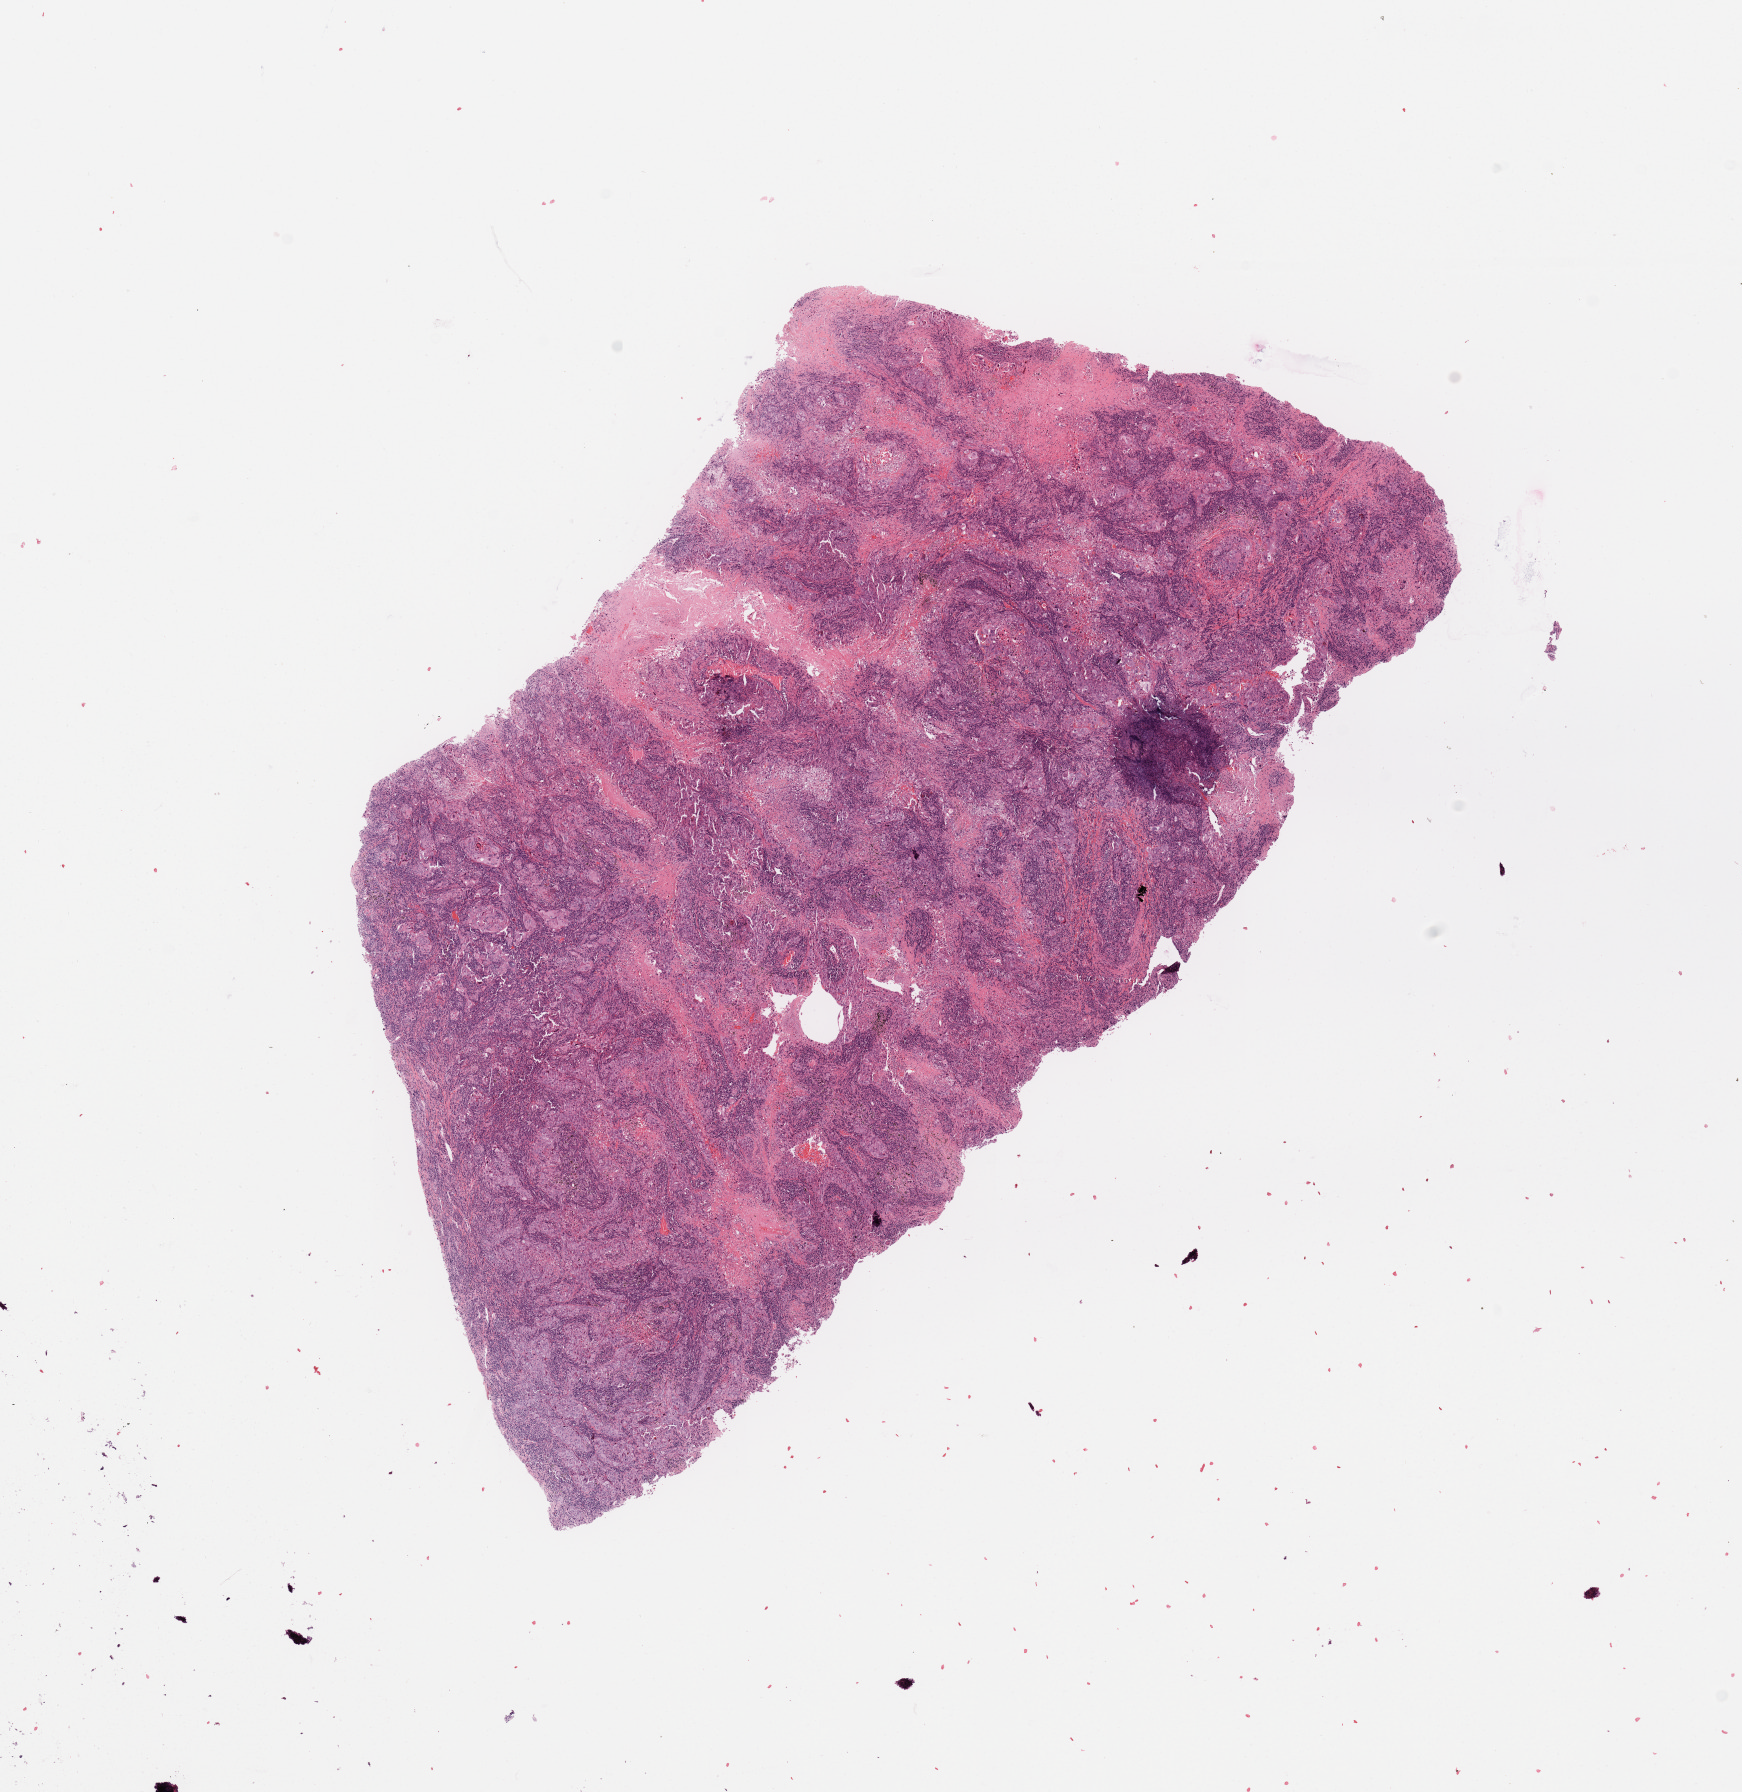
Digitized Hematoxylin and eosin (H&E) stained tissue section (whole slide), whole scanned area (about 13.8 x 14.2 mm) shown as a low-resolution overview. Tumour tissue sample, sampled site: lung. 64-year-old male patient. Pathologist review of this section (percent, as recorded): tumour nuclei 70%, necrosis 5%.
Histologic diagnosis: Adenocarcinoma, NOS.